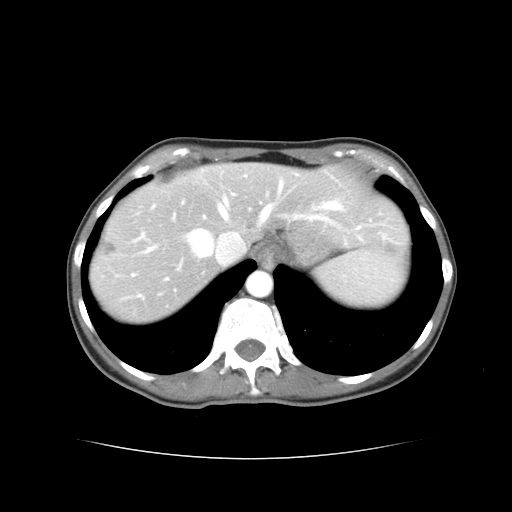
Contrast-enhanced abdominal CT, one axial slice; reconstruction kernel STANDARD; soft-tissue window (W 400 / L 40 HU); 5 mm slice thickness; 512 × 512 image matrix, field of view 340 × 340 mm. Female patient, age 54 years. Case-level facts recorded for this patient, not image findings: diagnosis: colorectal cancer liver metastases, imaged before liver resection; multiple liver metastases: yes; largest metastasis: 1.1 cm.
Structures marked on this image (outlined manually by an expert reader):
- hepatic veins: bounding box [x1, y1, x2, y2] px = [190, 183, 333, 256]
- liver: [91, 165, 405, 320]
- planned liver remnant (the part of the liver to remain after resection): [206, 165, 405, 248]
- portal vein (with intrahepatic branches): [143, 218, 265, 254]
- liver metastasis: [105, 242, 114, 255]